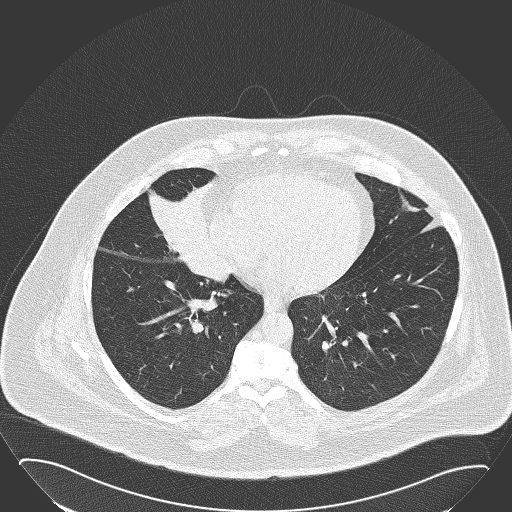
Low-dose screening chest CT, axial slice. Baseline screening round. Lung window (W 1500 / L -600 HU). Lung (sharp) reconstruction kernel (B50f). Male participant, aged 61 years at enrolment. Former smoker at enrolment.
• Lesion marked by an expert reader, bounding box (x1, y1, x2, y2) in pixels: (135, 176, 228, 265).
• The screening reader recorded 2 non-calcified nodules or masses ≥4 mm on this exam (right middle lobe, left lower lobe); which of them this box marks is not recorded.
• Participant outcome: lung cancer diagnosed 47 days after this screen — basaloid squamous cell carcinoma, right middle lobe, right hilum, poorly differentiated (G3), stage IIB (AJCC 6th edition), 95 mm at pathology.